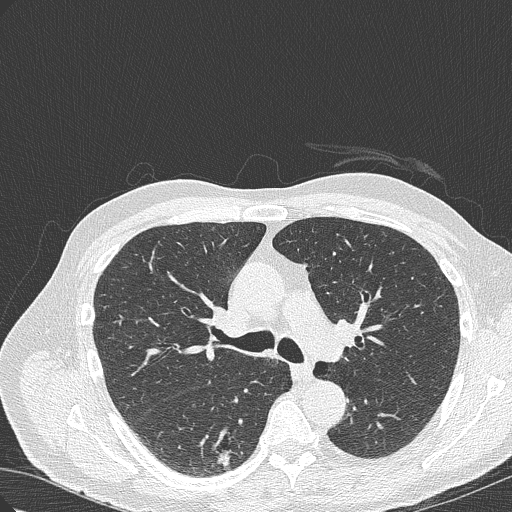
Chest CT (low-dose screening protocol), one axial image. Baseline screening round. Lung window (W 1500 / L -600 HU). Lung (sharp) reconstruction kernel (B50f). Slice 116 of 322 in the series. Male, age 70 years at enrolment. Current smoker at enrolment.
Expert-annotated lung lesion, bounding box <201,419,265,468> (left, top, right, bottom; pixels). The screening reader recorded 4 non-calcified nodules or masses ≥4 mm on this exam; which of them this box marks is not recorded. Official screen result: positive, change unspecified: nodule(s) >= 4 mm or enlarging nodule(s), mass(es), or other non-specific abnormalities suspicious for lung cancer. Participant outcome: lung cancer diagnosed 978 days after this screen (after the third annual screen) — bronchiolo-alveolar adenocarcinoma, NOS, right lower lobe, poorly differentiated (G3), stage IB (AJCC 6th edition), 30 mm at pathology.